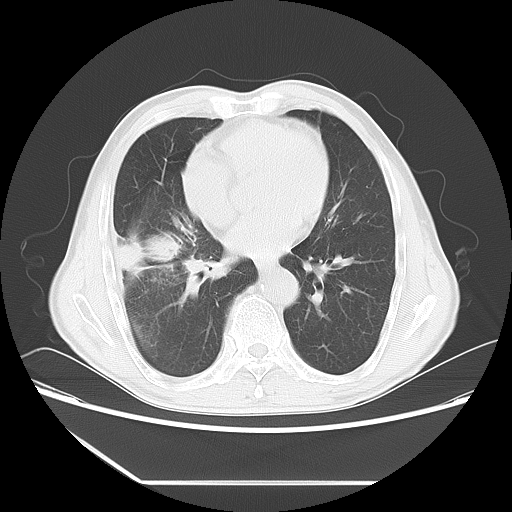
Chest CT, one axial slice. Position 26 of 60 along the scan axis. 120 kVp. Lung window (W 1500 / L -600 HU). 5 mm slice thickness. 512 × 512 image matrix, field of view 386 × 386 mm. Patient: male, 72 years. From the clinical record (not read from this slice): clinical TNM (as recorded): T1c N0 M0.
Structures marked on this image (bounding box drawn by a radiologist):
- lung tumour (recorded histology: squamous cell carcinoma): box from (x=117, y=225) to (x=195, y=274) px